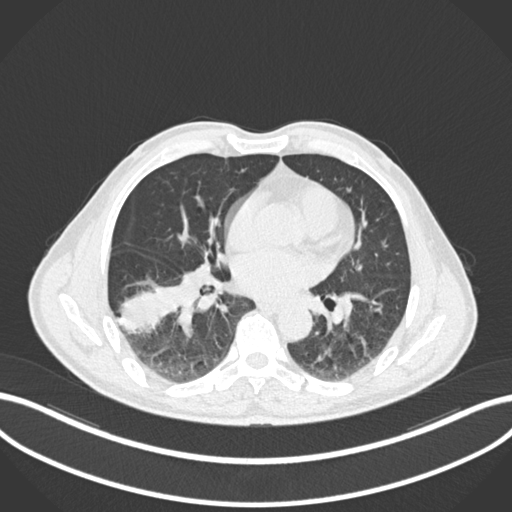
Chest CT, one axial slice; slice 90 of 208 in the series (ordered by position); 120 kVp; lung window (W 1500 / L -600 HU); 1 mm slice thickness; 512 × 512 image matrix, field of view 400 × 400 mm. Patient: male, 58 years. From the clinical record (not read from this slice): clinical TNM (as recorded): T3 N0 M0; histopathological grade: G2.
Annotated regions visible in this slice (rectangle marked by the reading radiologist):
- lung tumour (recorded histology: squamous cell carcinoma): bounding box [x1, y1, x2, y2] px = [116, 275, 179, 335]